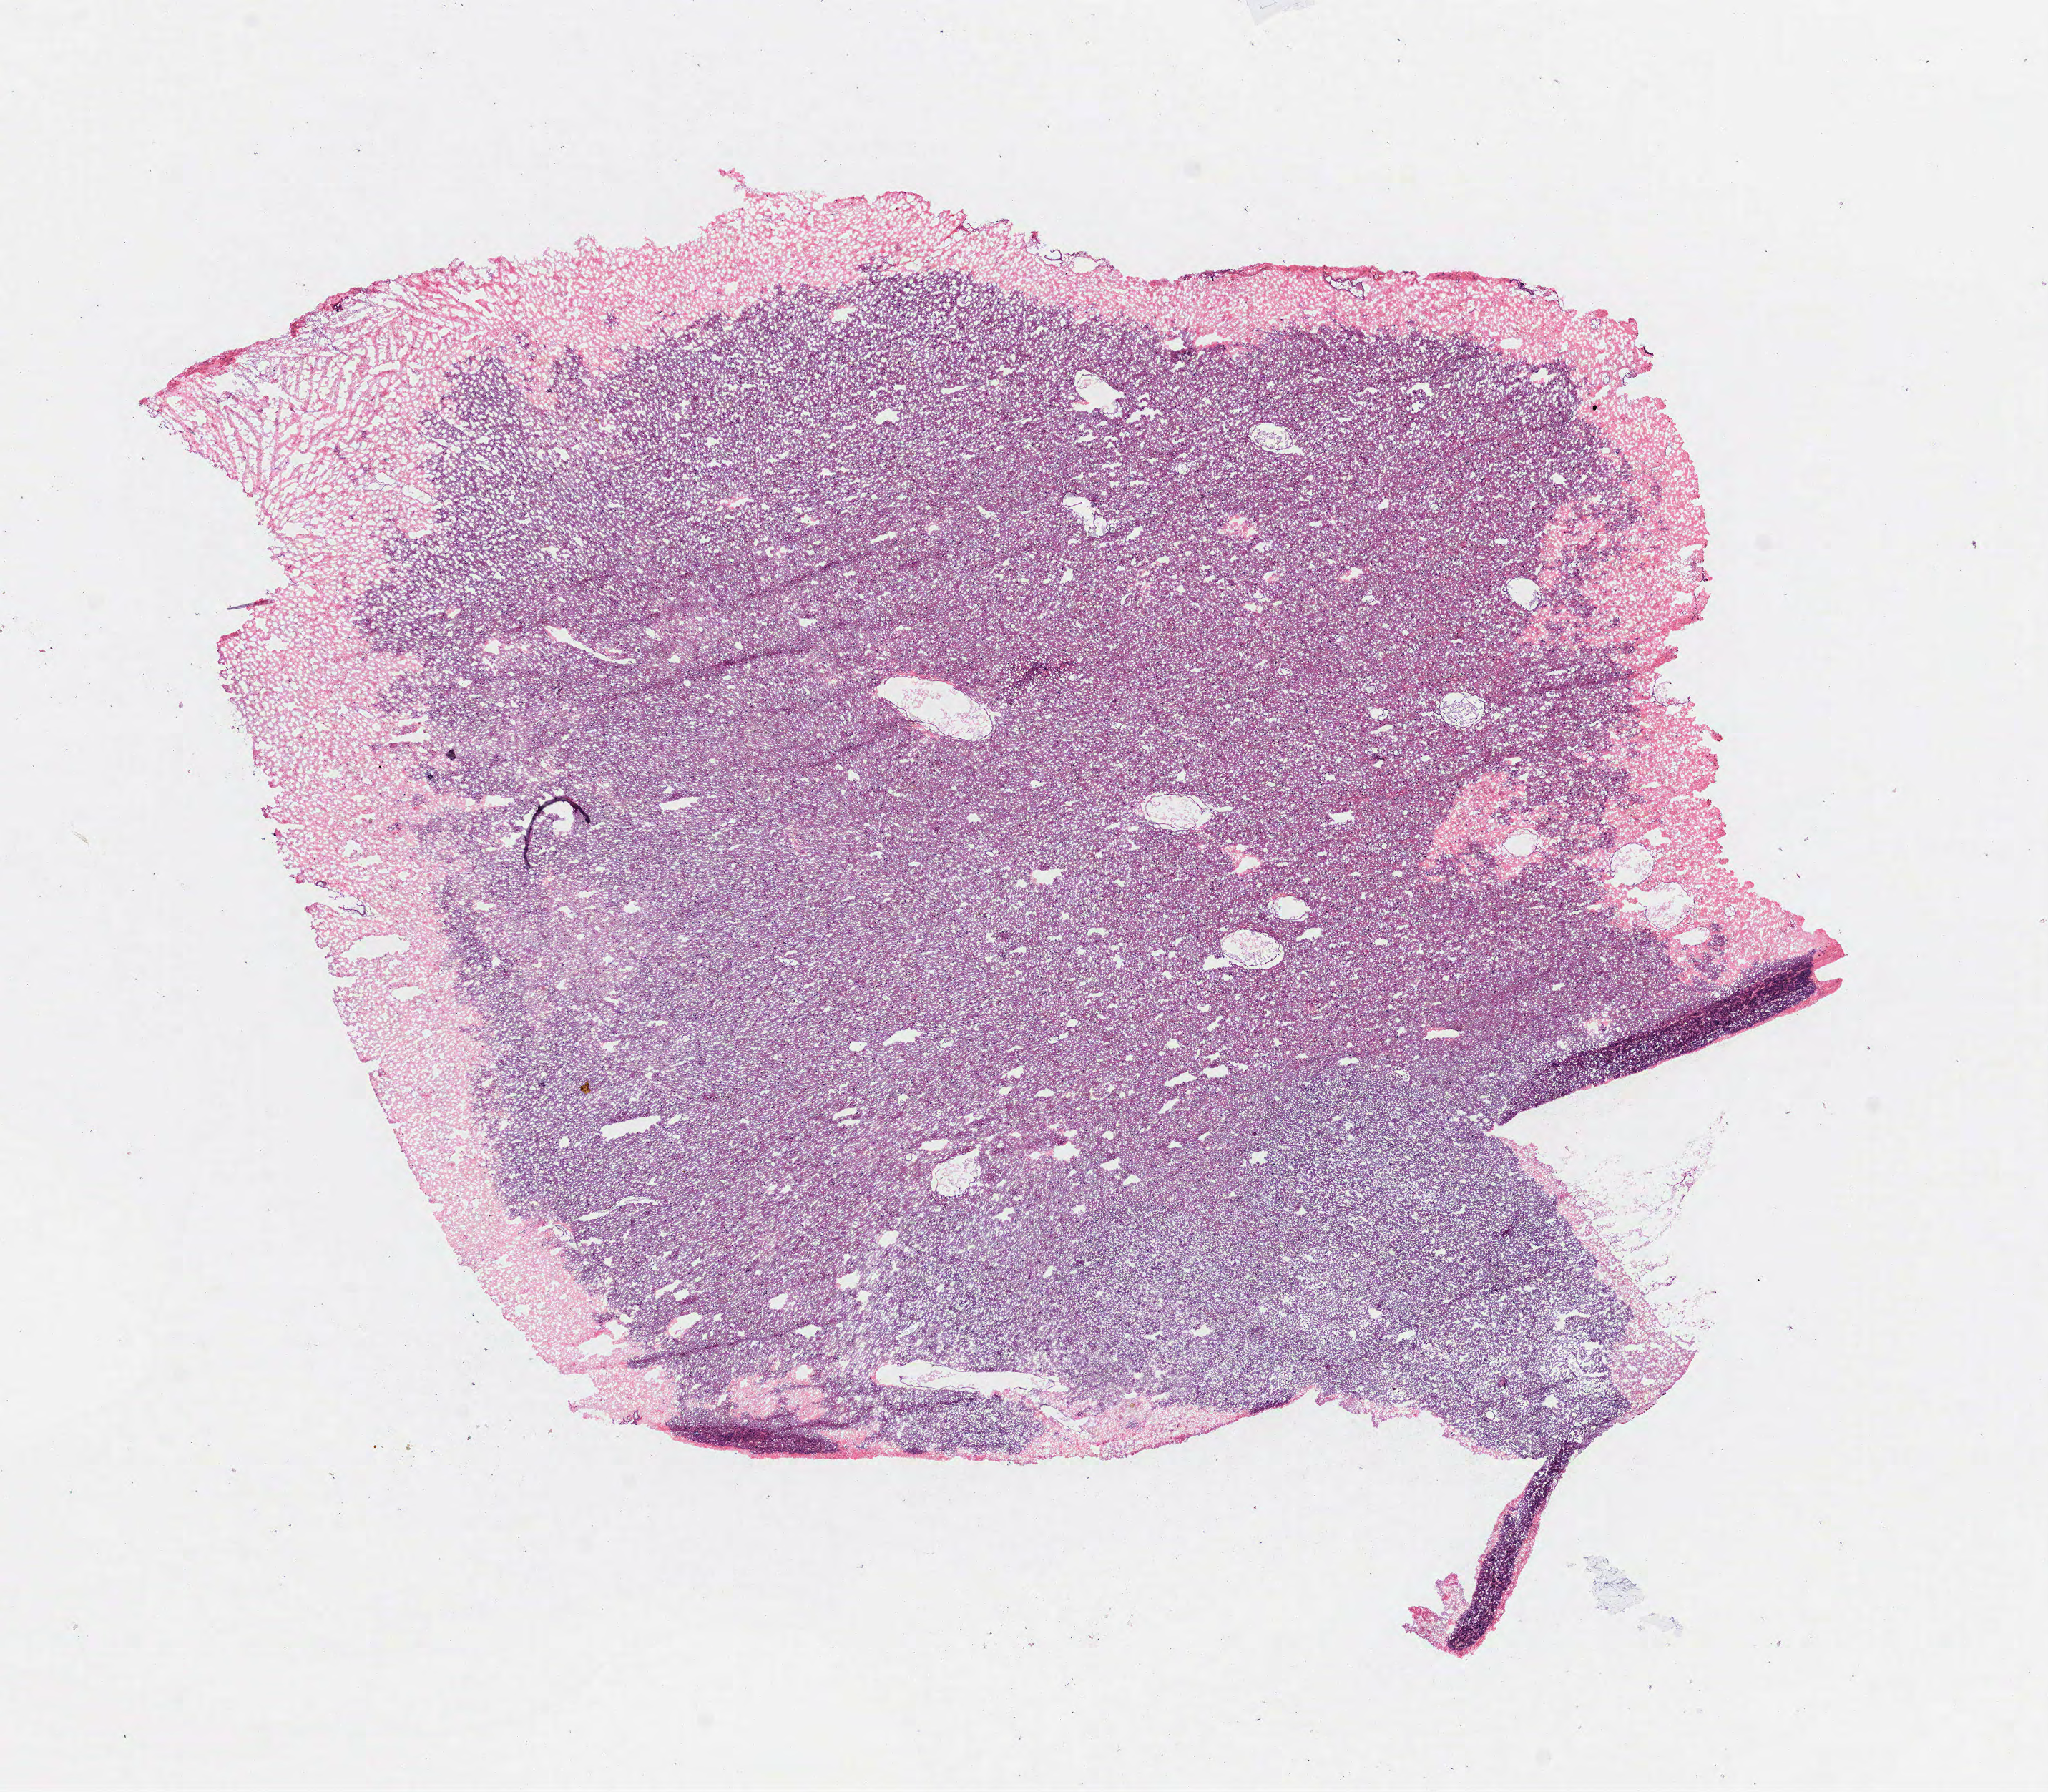
H&E whole-slide image — whole scanned area (about 11.5 x 10.1 mm, from a 40x scan) shown as a low-resolution overview; frozen section from the top of the tissue portion; brain, primary tumour sample. Male, age 38 years at initial diagnosis. Histologic grade: G2 (moderately differentiated). Composition of this section per pathologist review: tumour cells 100%, tumour nuclei 65%, normal cells 0%, stromal cells 0%, necrosis 0%.
Diagnosis: Oligodendroglioma, NOS (cerebrum).